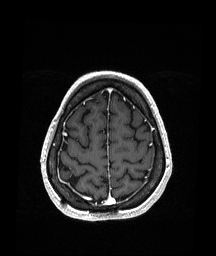
Brain MRI from a brain-tumour surgery series, one axial slice. Position 50 of 151 along the scan axis. T1-weighted post-contrast. 1.05 mm slice thickness. 216 × 256 image matrix, field of view 211 × 250 mm. From the clinical record (not read from this slice): histopathology: Oligodendroglioma; WHO grade: 2; IDH mutation: yes.
Outlined on this slice (outlined manually by an expert reader):
- previous resection cavity: box from (x=105, y=179) to (x=108, y=181) px